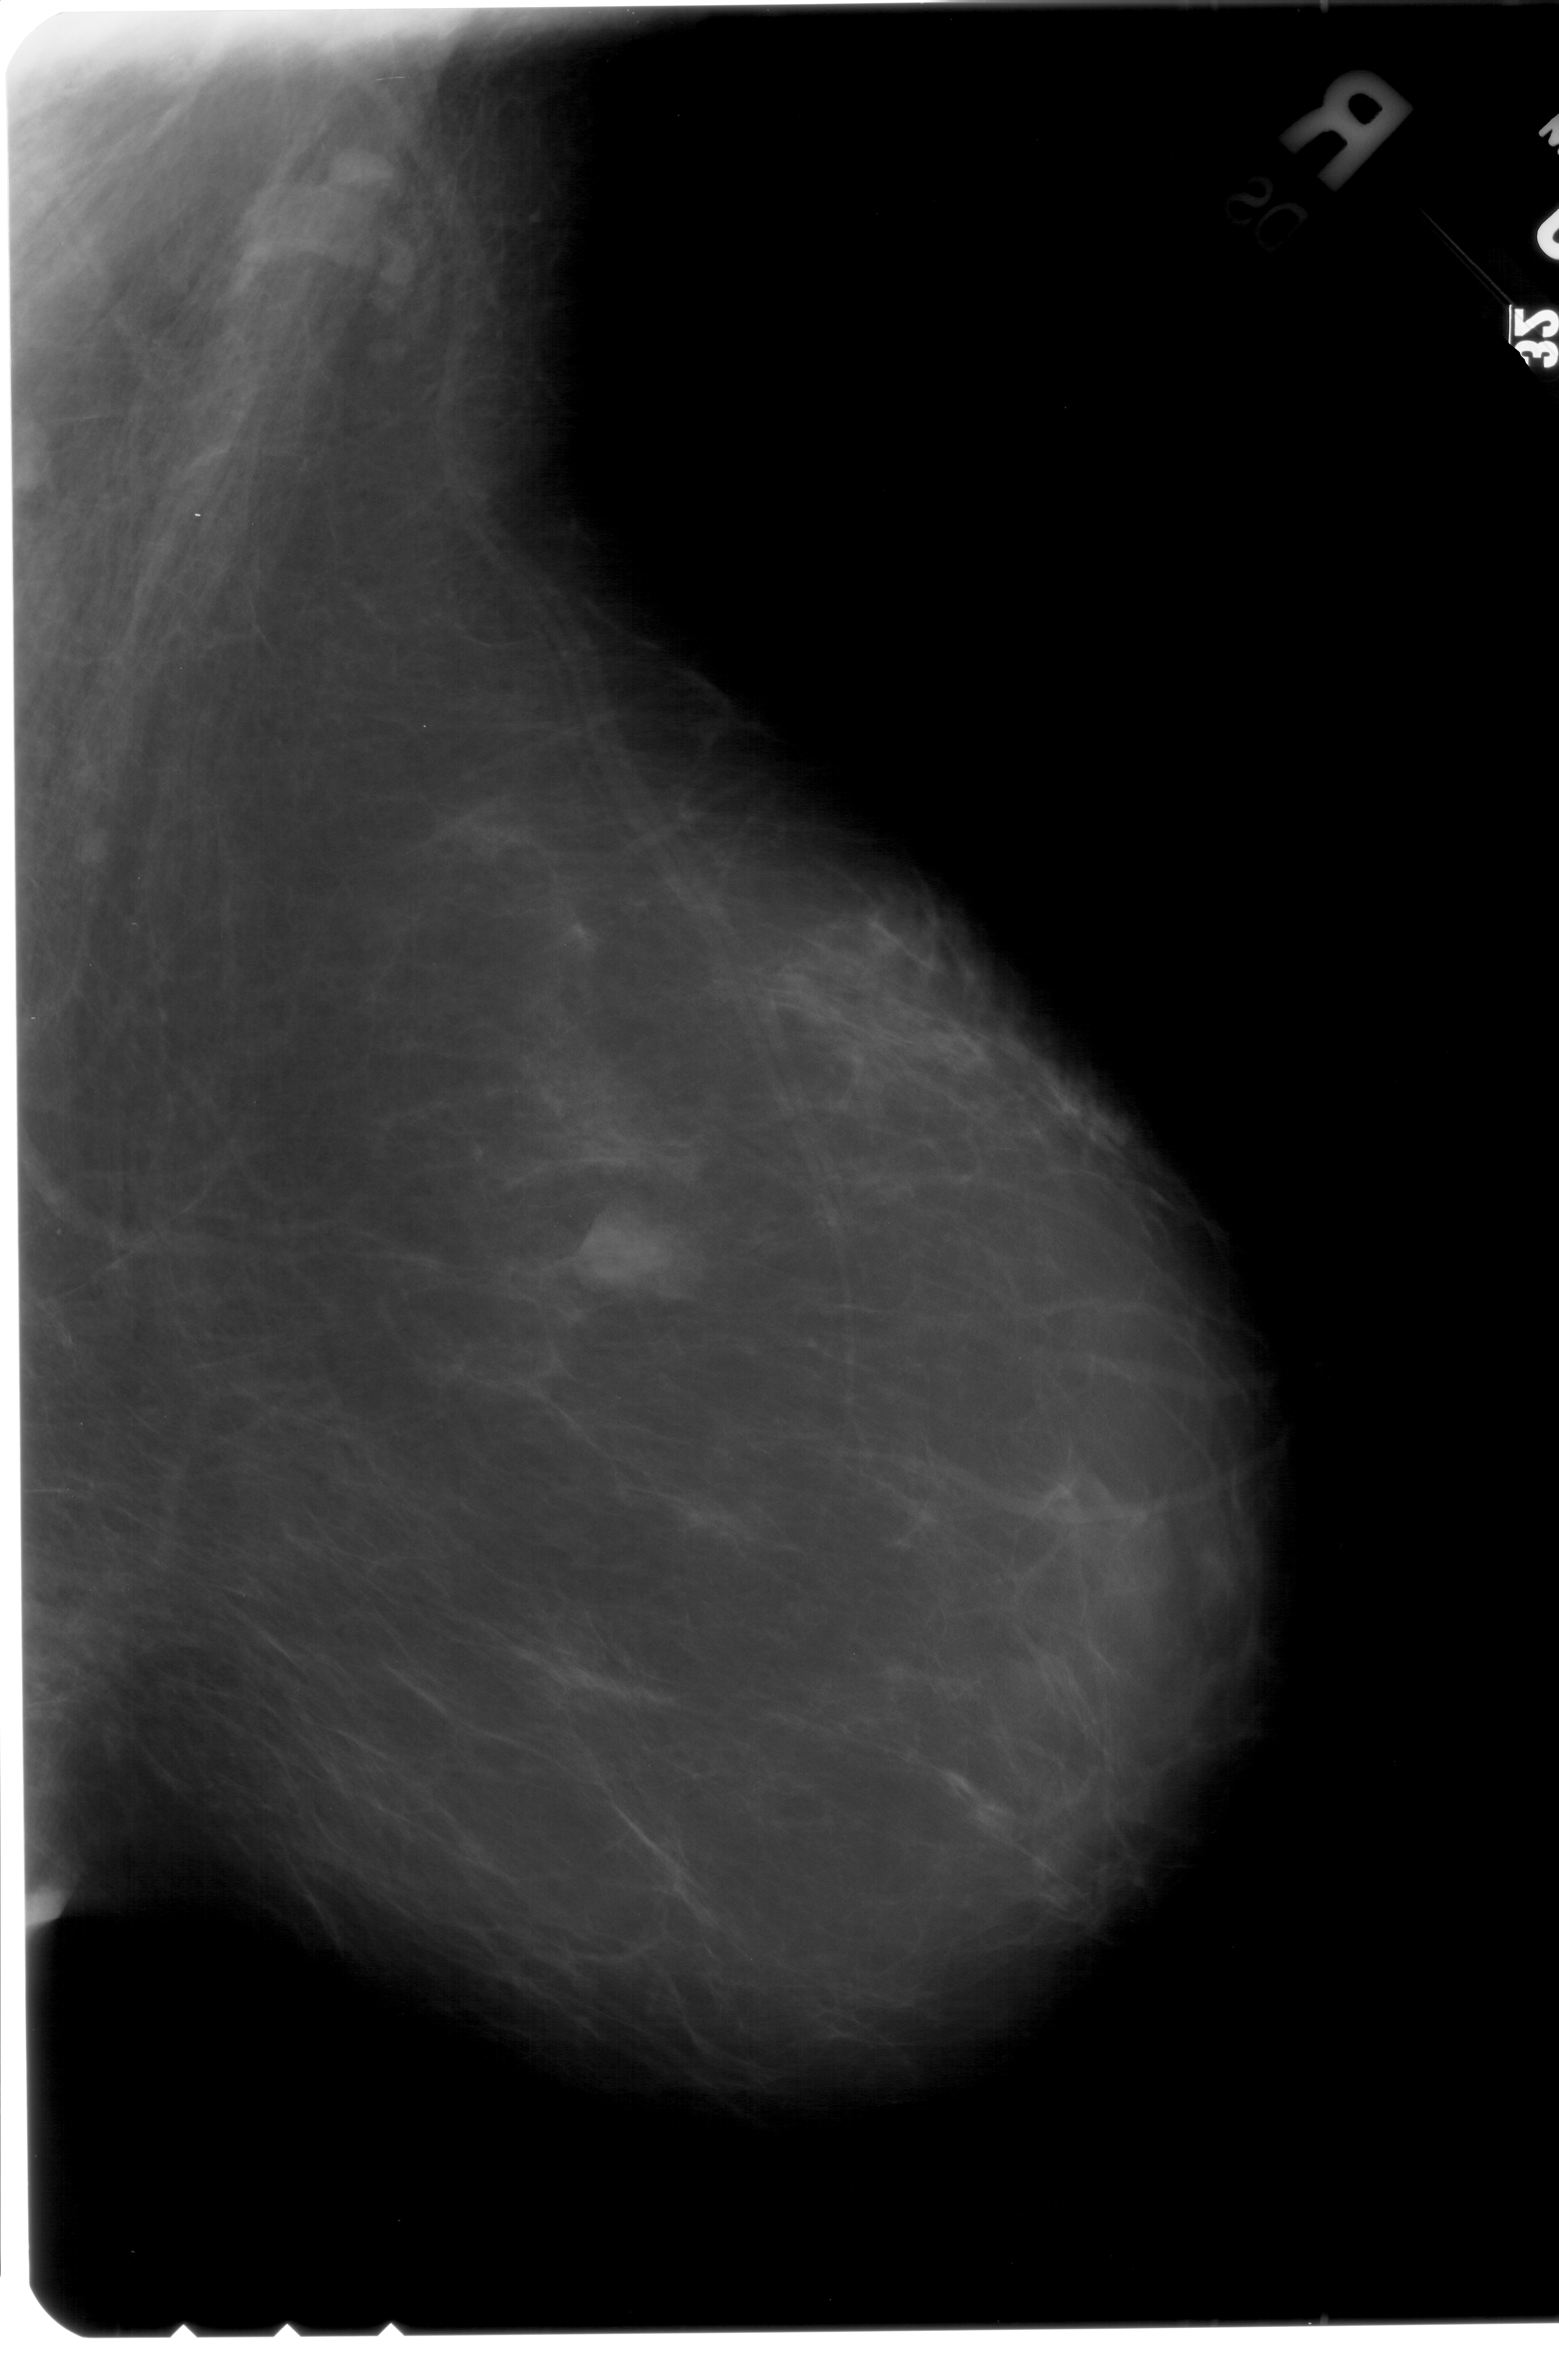
Scanned film-screen mammogram; right breast; mediolateral oblique (MLO) view; breast composition: scattered fibroglandular densities (BI-RADS density category 2 of 4); 1559 × 2380 image matrix.
Expert-marked regions of interest on this film, with their recorded descriptors:
- mass, shape lobulated, margins circumscribed; BI-RADS assessment category 4; pathology result (as recorded, not read from the image): benign: bounding box (x1, y1, x2, y2) in pixels: (562, 1202, 697, 1302)